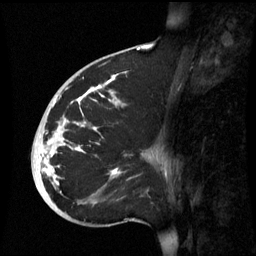
Breast MRI (dynamic contrast-enhanced), one sagittal slice. Dynamic contrast-enhanced series, image 2 of 3 at this slice position (ordered by acquisition). 1.5 T. TE 4.2 ms, TR 8.9 ms. 256 × 256 image matrix. Patient: female, 35 years. Case-level facts recorded for this patient, not image findings: setting: breast cancer imaged before/during neoadjuvant chemotherapy; receptor status: HR-positive, HER2-negative.
Annotated regions visible in this slice (semi-automatic segmentation, software-assisted and operator-edited):
- analysis volume of interest (the breast-tissue region the enhancement analysis was run in; not a lesion): bounding box (x1, y1, x2, y2) in pixels: (32, 74, 164, 221)
- tumour enhancement mask (voxels above the 70 % enhancement threshold inside the analysis volume of interest): (39, 74, 118, 185)